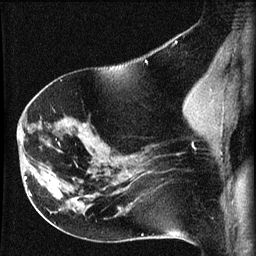
Breast MRI (dynamic contrast-enhanced), one sagittal slice. Position 37 of 60 along the scan axis. Dynamic contrast-enhanced series, image 2 of 3 at this slice position (ordered by acquisition). 1.5 T. TE 4.2 ms, TR 8.2 ms. 2 mm slice thickness. 256 × 256 image matrix. Patient: female, 63 years.
Structures marked on this image (semi-automatically segmented with operator editing):
- analysis volume of interest (the breast-tissue region the enhancement analysis was run in; not a lesion): bounding box [x1, y1, x2, y2] px = [22, 156, 64, 202]
- tumour enhancement mask (voxels above the 70 % enhancement threshold inside the analysis volume of interest): [24, 176, 59, 193]